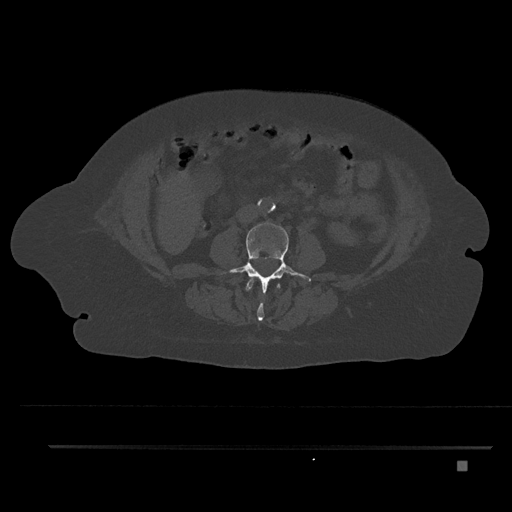
CT including the spine, one axial slice; slice 129 of 797 in the series (ordered by position); reconstruction kernel Br40s/3; 120 kVp; bone window (W 1800 / L 400 HU); 0.5 mm slice thickness; 512 × 512 image matrix, field of view 437 × 437 mm. Patient: female, 76 years. Case-level facts recorded for this patient, not image findings: primary cancer: lung.
Annotated regions visible in this slice (semi-automatic segmentation, software-assisted and operator-edited):
- L2 vertebra: bounding box (x1, y1, x2, y2) in pixels: (245, 278, 281, 321)
- L3 vertebra: (220, 222, 311, 293)